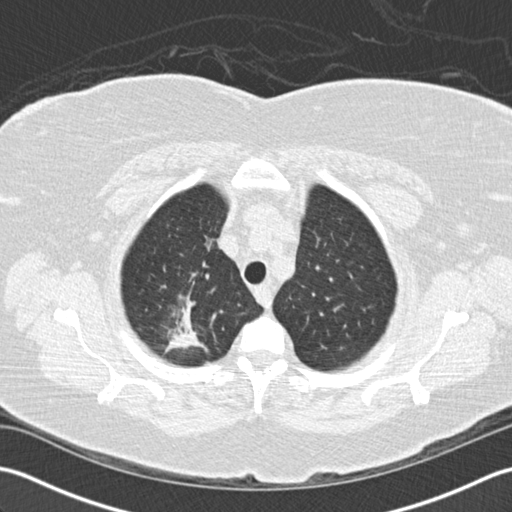
Axial slice from a low-dose chest CT screening exam. Baseline annual screen. Lung window (W 1500 / L -600 HU). 120 kVp. 512 × 512 image matrix, field of view 350 × 350 mm. Female, age 72 years at enrolment. Former smoker at enrolment.
Expert reader's lesion annotation, bounding box (x1, y1, x2, y2) in pixels: (136, 276, 228, 367). The screening reader recorded 2 non-calcified nodules or masses ≥4 mm on this exam (right lower lobe, right lower lobe); which of them this box marks is not recorded. Lung cancer was diagnosed 494 days after this screen (after the second annual screen): bronchiolo-alveolar adenocarcinoma, NOS, right upper lobe, stage IIIB (AJCC 6th edition), 45 mm at pathology.